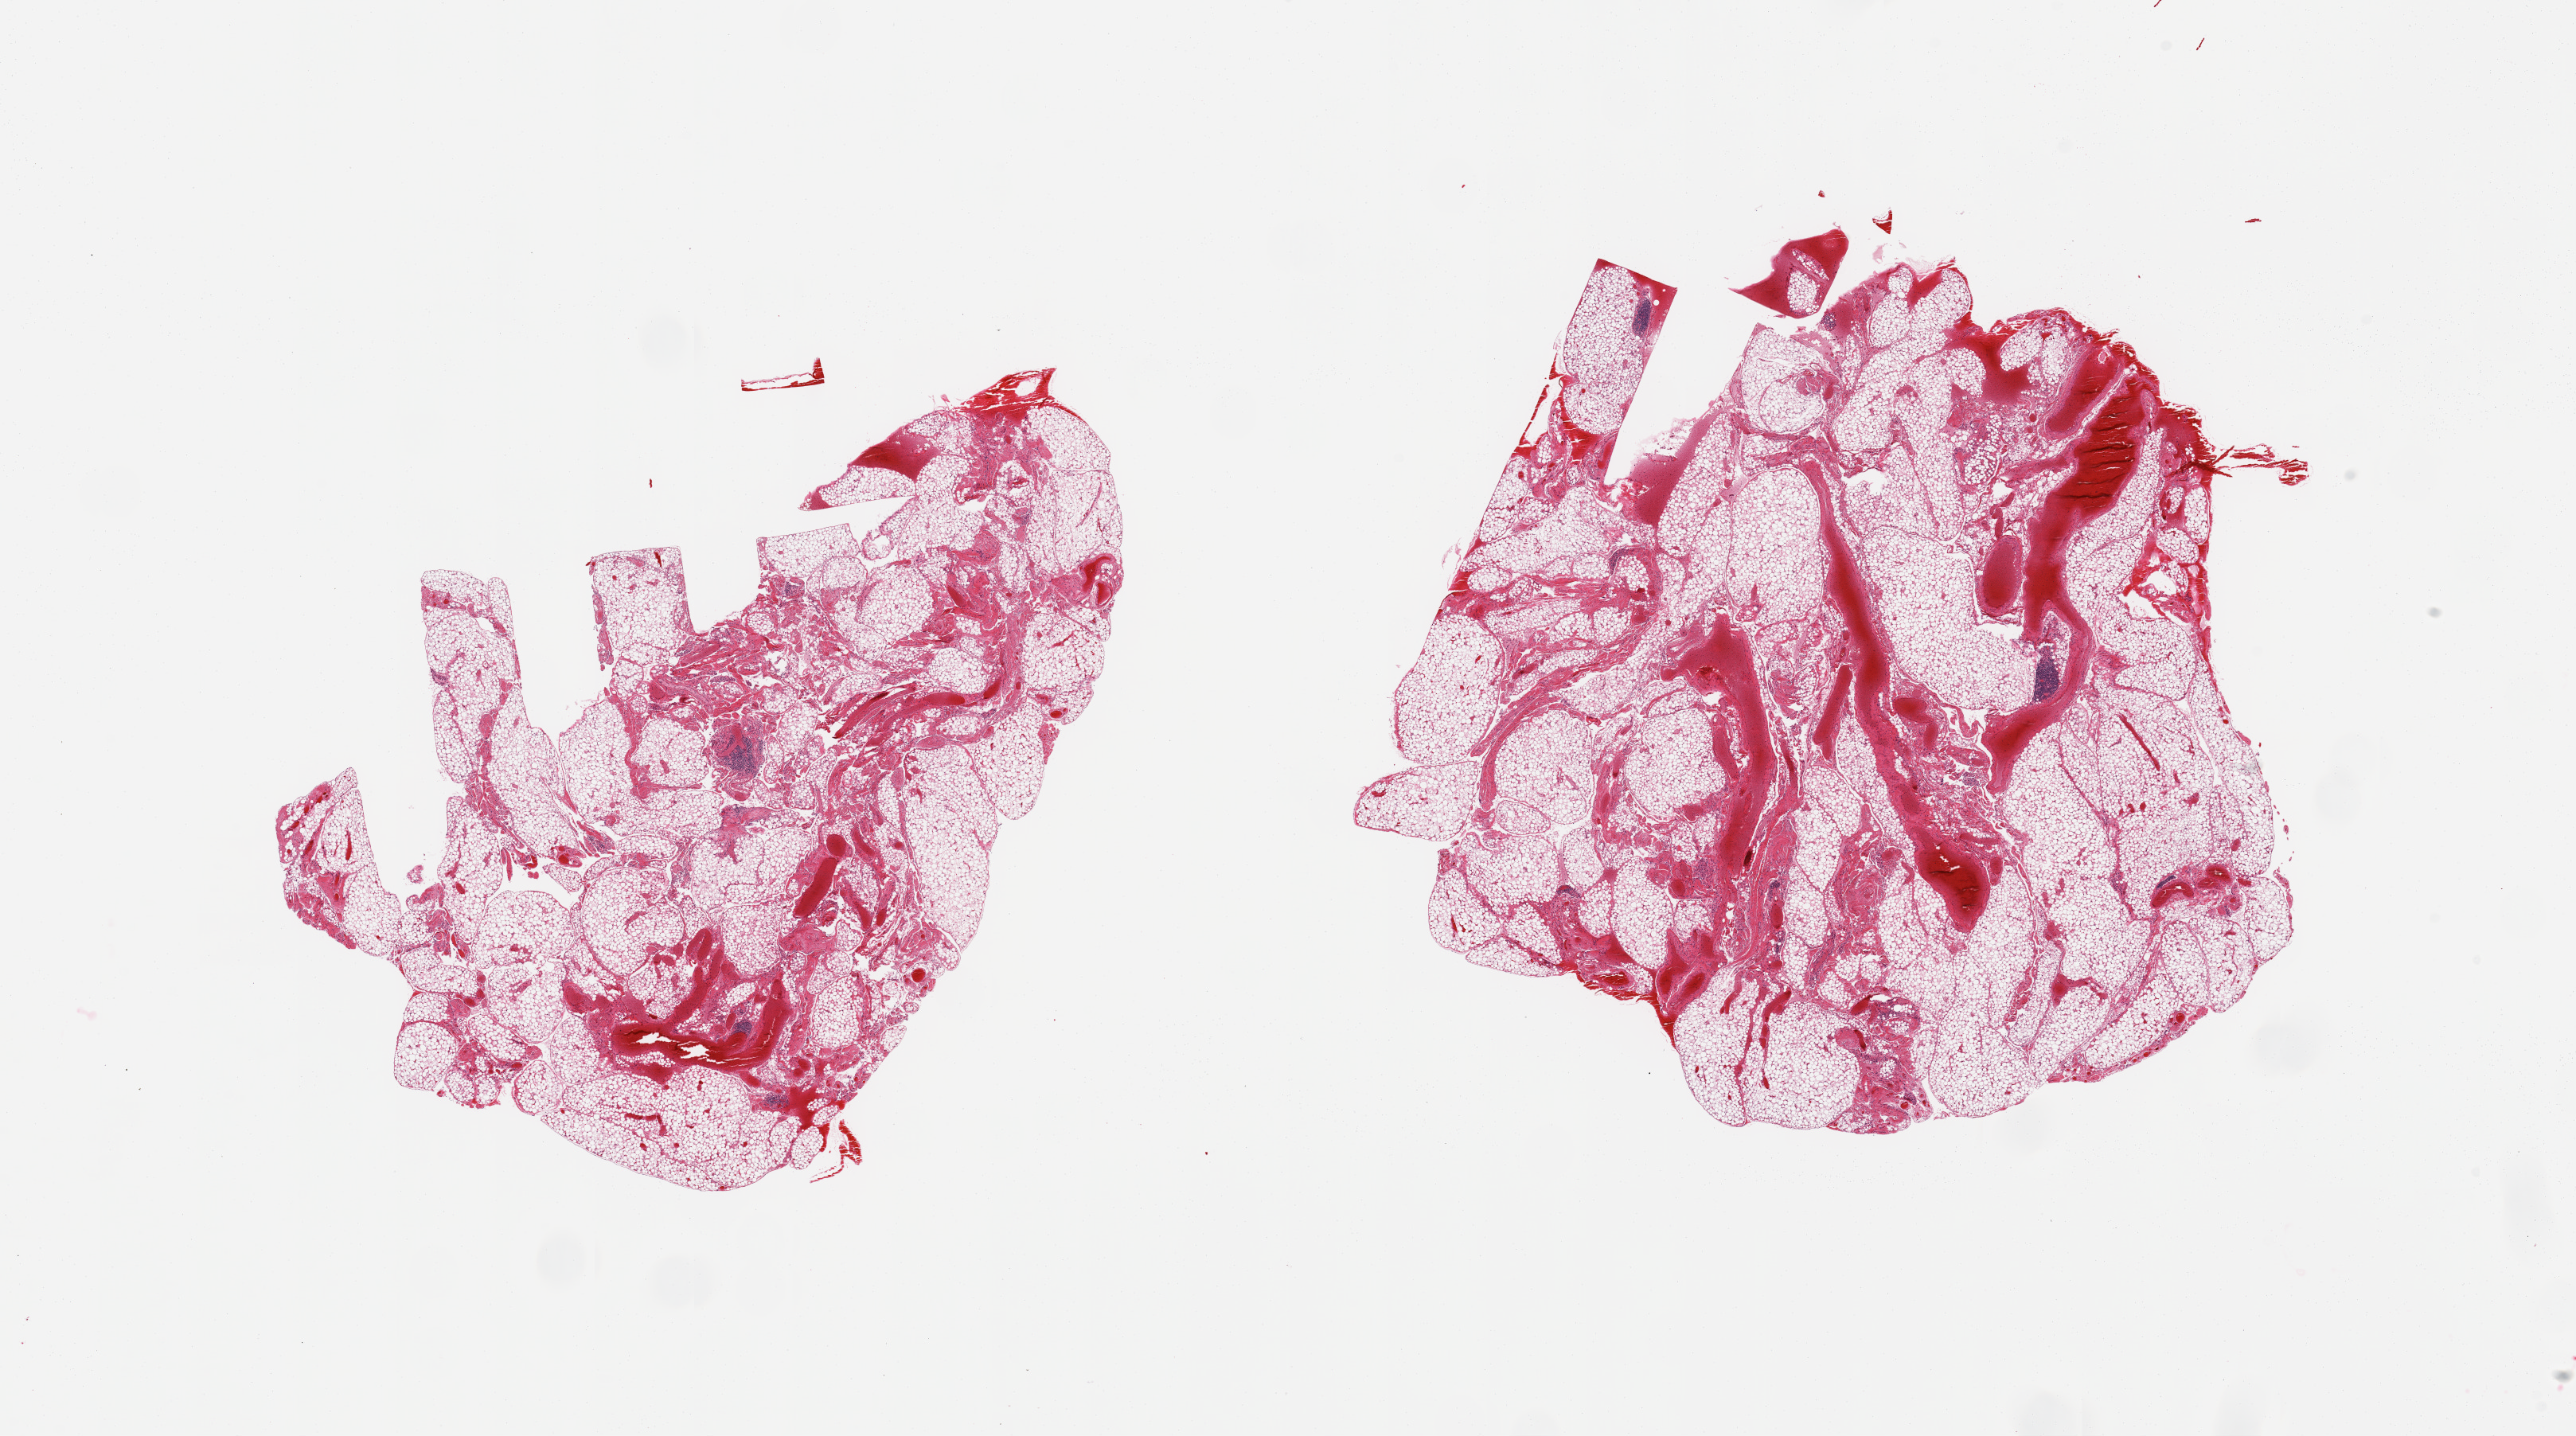
Haematoxylin and eosin whole-slide image, shown as a low-resolution overview of the whole scanned area (about 25.6 x 14.3 mm), PAXgene-fixed, paraffin-embedded tissue, target tissue: omentum, tissue donor sample. Male donor.
Pathologist's review note for this sample: 2 pieces; lobulated mature adipose tissue with marlkedly congested fibrovascular component; sparse small.